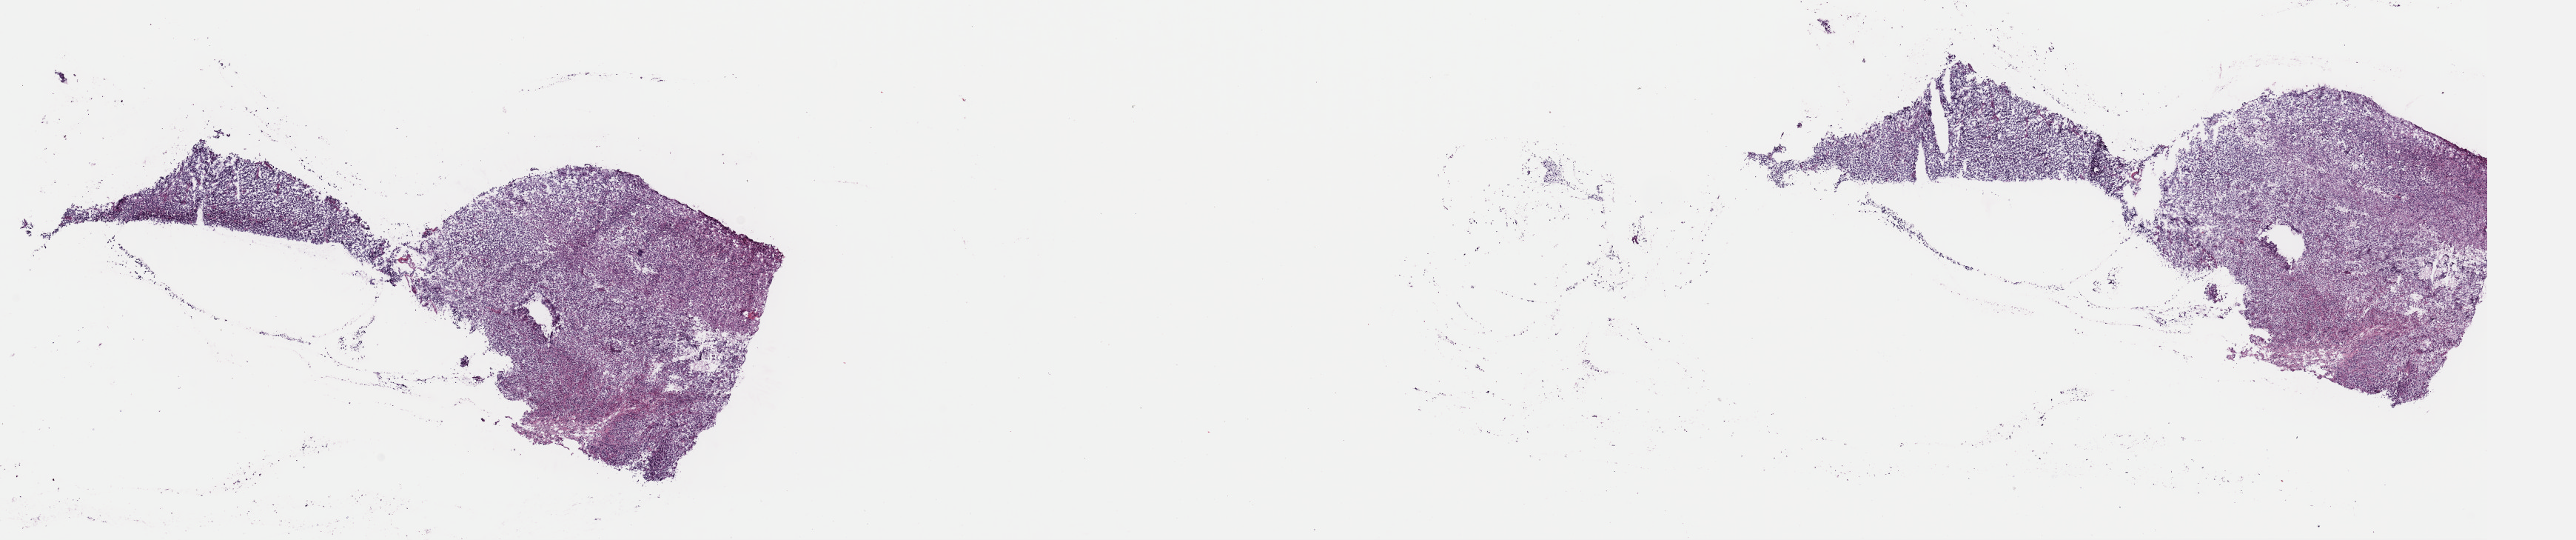
Digitized H&E tissue section (whole slide) — shown as a low-resolution overview of the whole scanned area (about 27.5 x 5.8 mm). Frozen section. Sample: recurrent tumour, brain. Male, age 45 years at initial diagnosis. Composition of this section per pathologist review: tumour cells 90%, tumour nuclei 90%, normal cells 0%, stromal cells 10%, necrosis 0%. Inflammatory infiltration, as recorded: lymphocyte infiltration 0%, monocyte infiltration 0%, neutrophil infiltration 0%.
This section: recurrent tumour. Patient diagnosis: Oligodendroglioma, anaplastic (cerebrum).